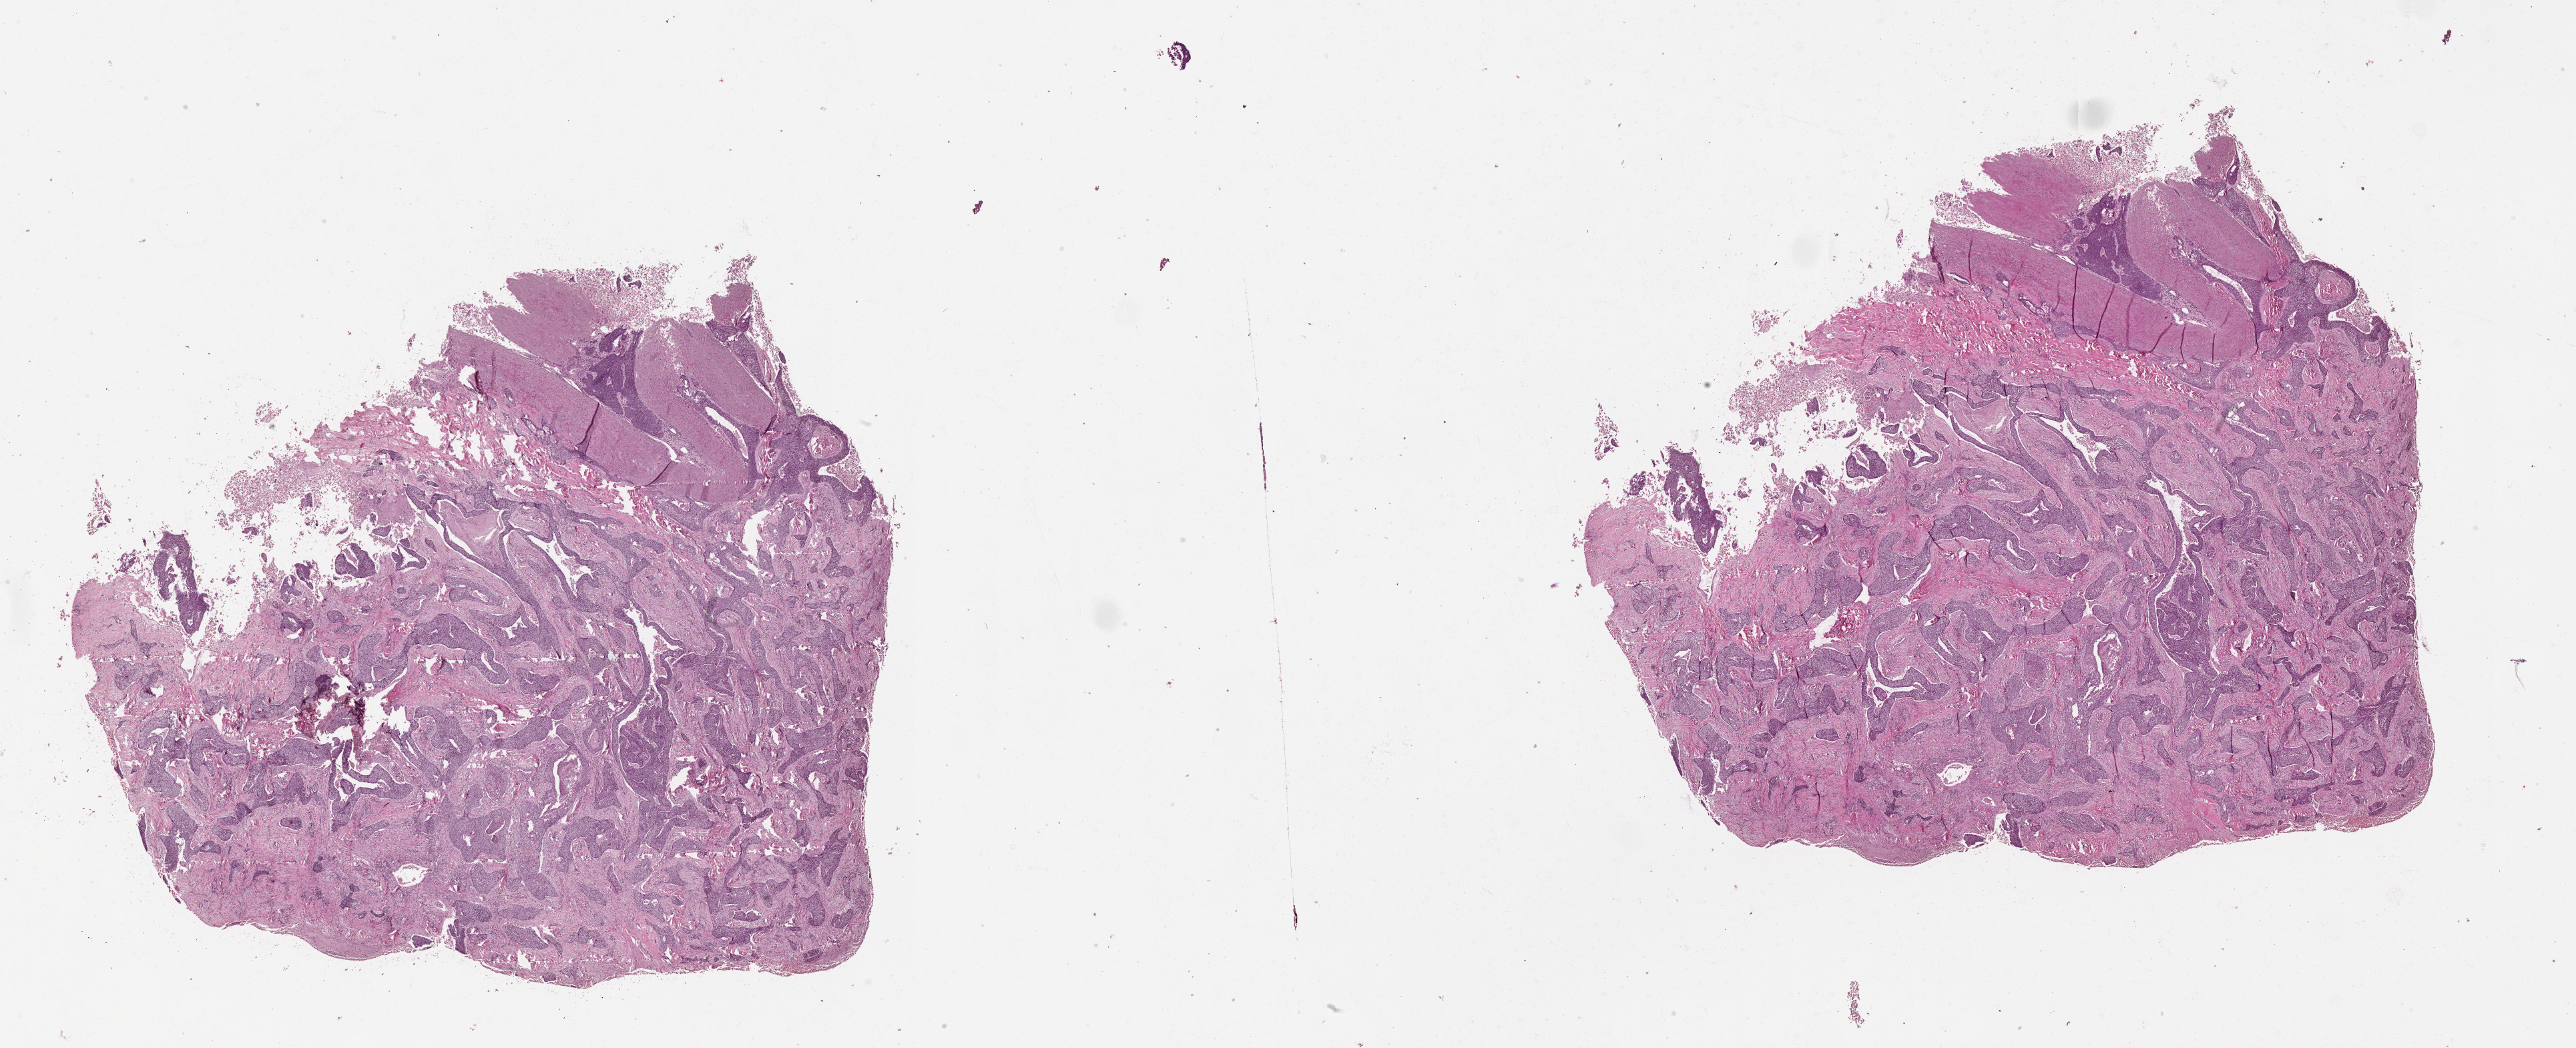
H&E whole-slide image, whole scanned area (about 31.1 x 12.6 mm, slide scanned at 20x) shown as a low-resolution overview. Lung, tumour tissue. Male, 63 y/o.
Patient diagnosis (cohort enrolment): squamous cell carcinoma (lung).